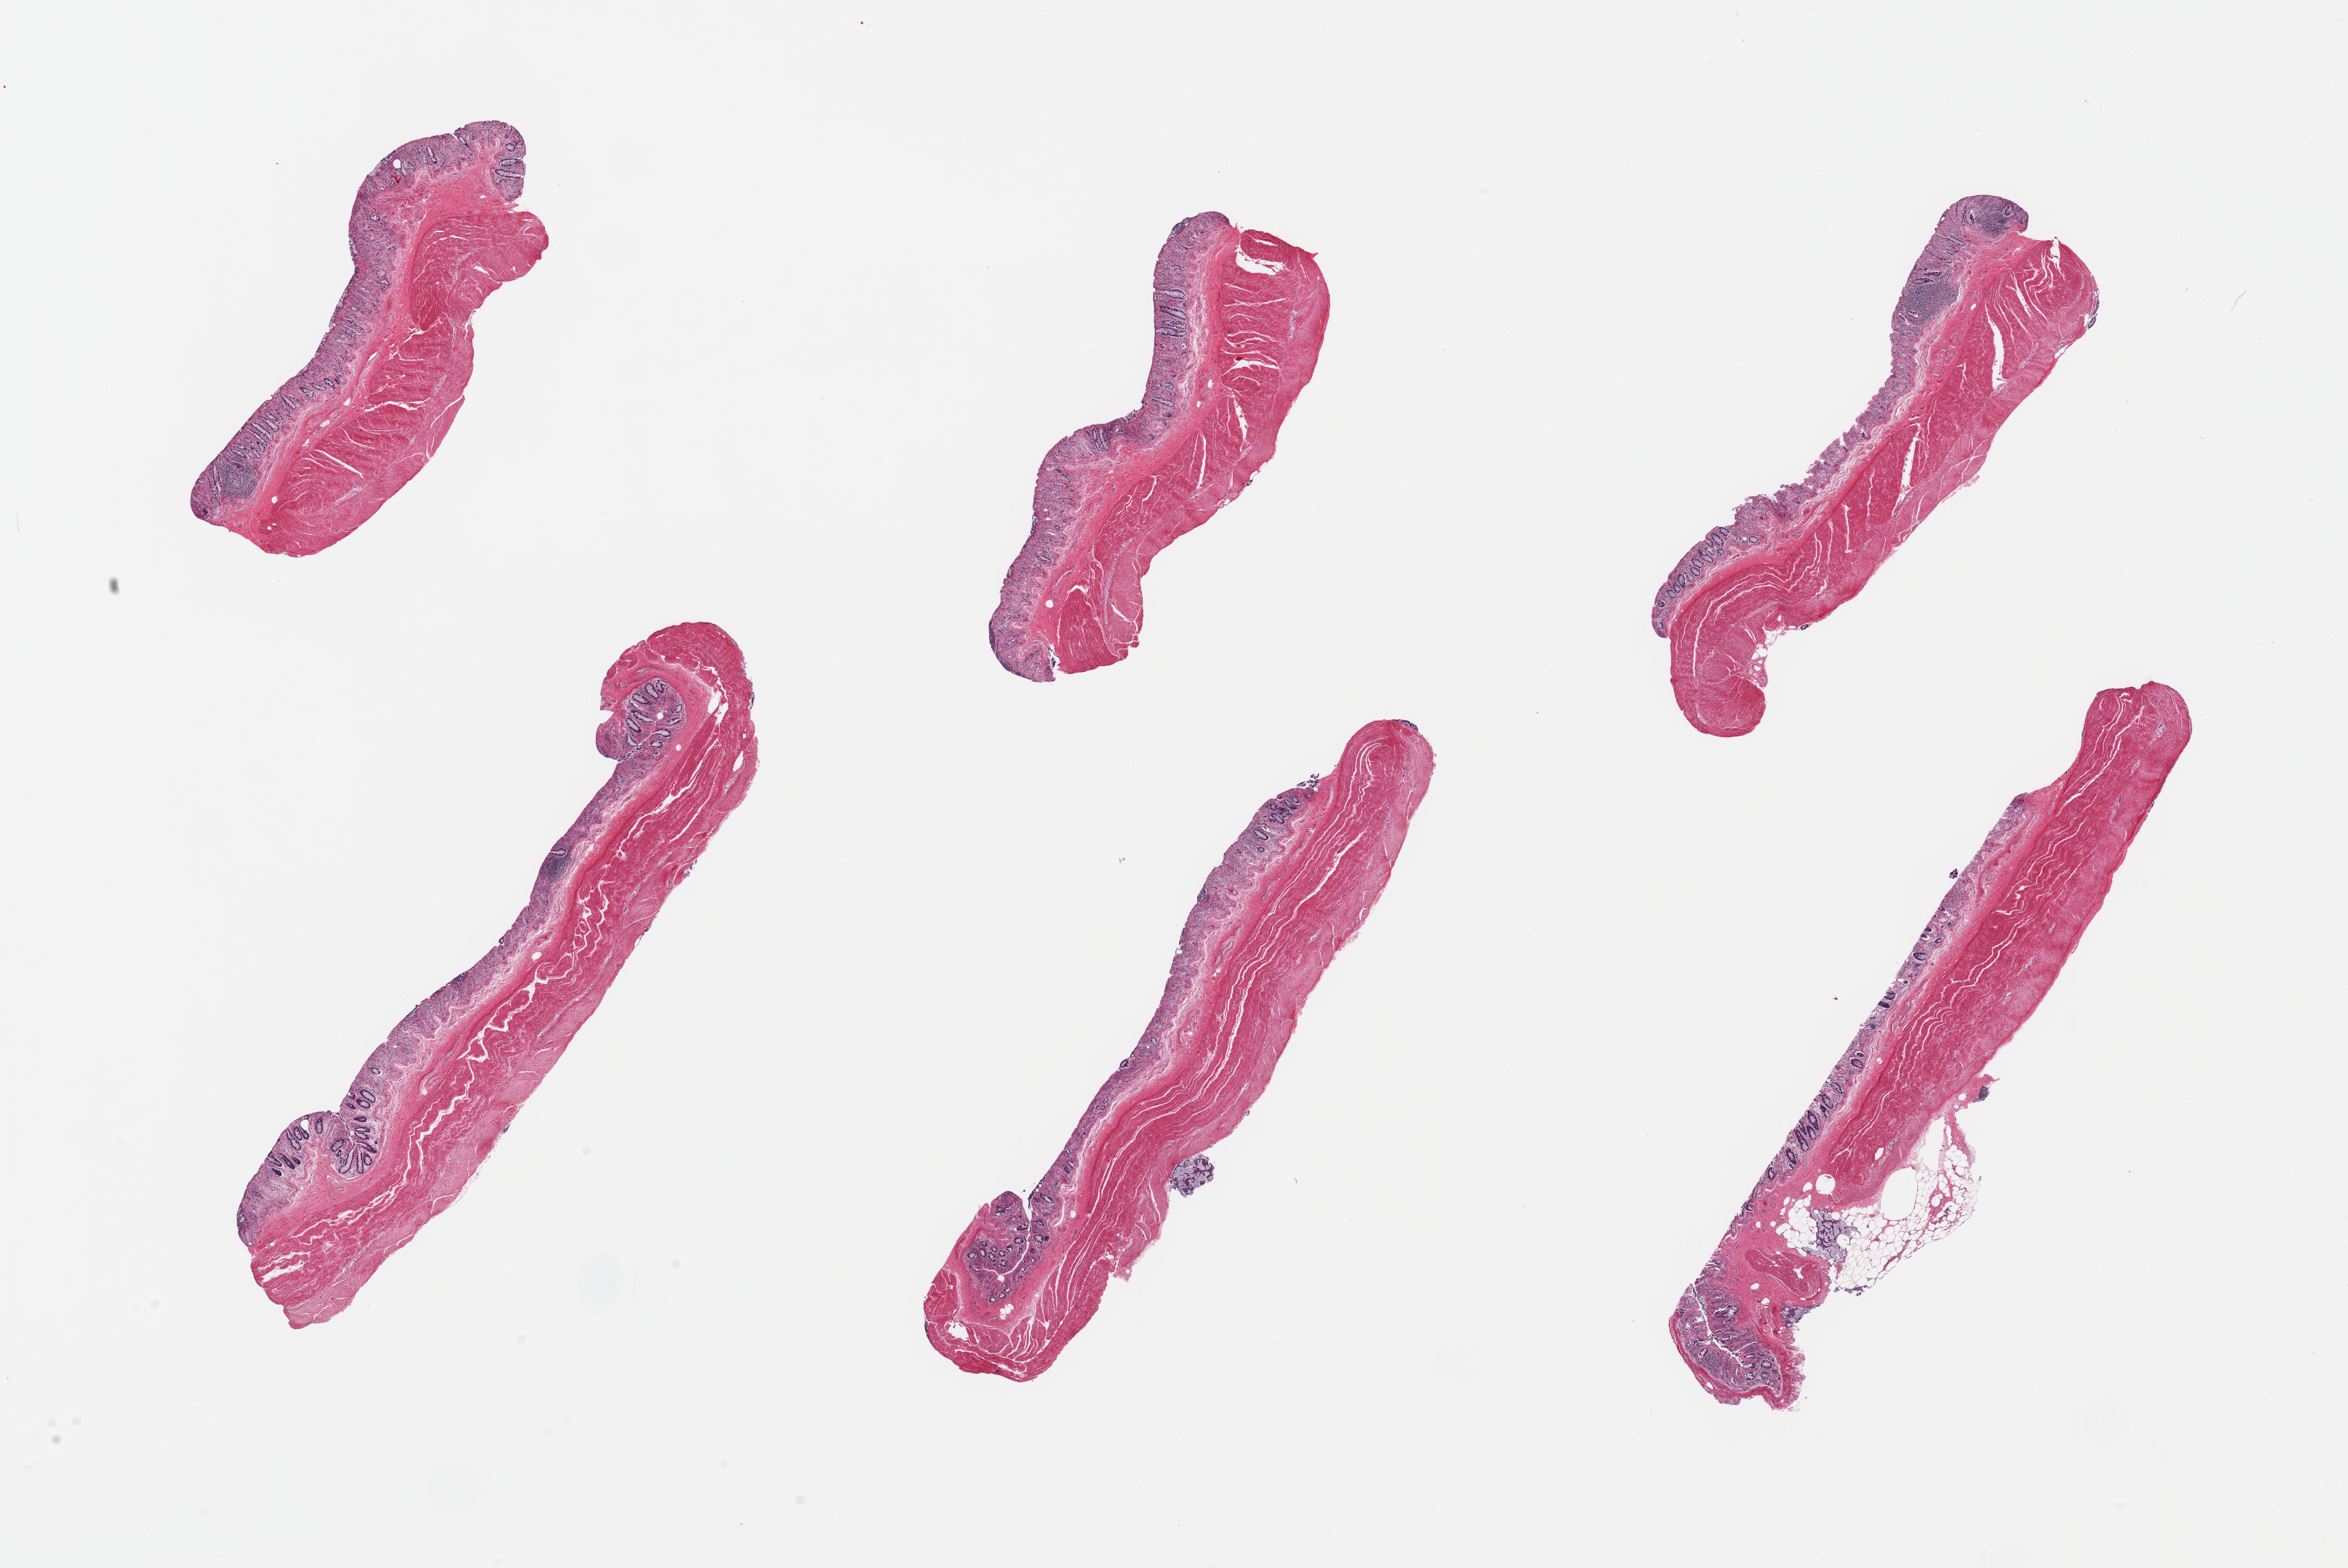
Hematoxylin and eosin (H&E) whole-slide image, whole scanned area (about 25.6 x 17.1 mm) shown as a low-resolution overview; PAXgene-fixed, paraffin-embedded tissue; target tissue: transverse colon; donor tissue sample. Donor: male.
Pathologist's review note for this sample: 6 pieces, target mucosa up to ~0.3mm; advanced glandular autolysis.